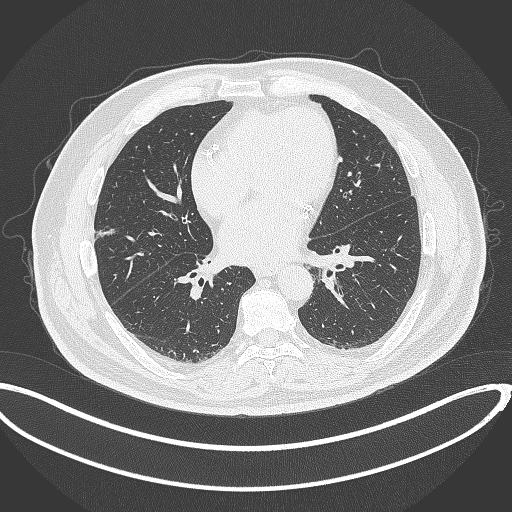
Chest CT, one axial slice; slice 144 of 340 in the series (ordered by position); 120 kVp; lung window (W 1500 / L -600 HU); 1 mm slice thickness; 512 × 512 image matrix. Male patient, age 68 years. Case-level facts recorded for this patient, not image findings: clinical TNM (as recorded): T1c N0 M0; histopathological grade: G2.
Structures marked on this image (bounding box drawn by a radiologist):
- lung tumour (recorded histology: adenocarcinoma): box from (x=93, y=226) to (x=116, y=239) px